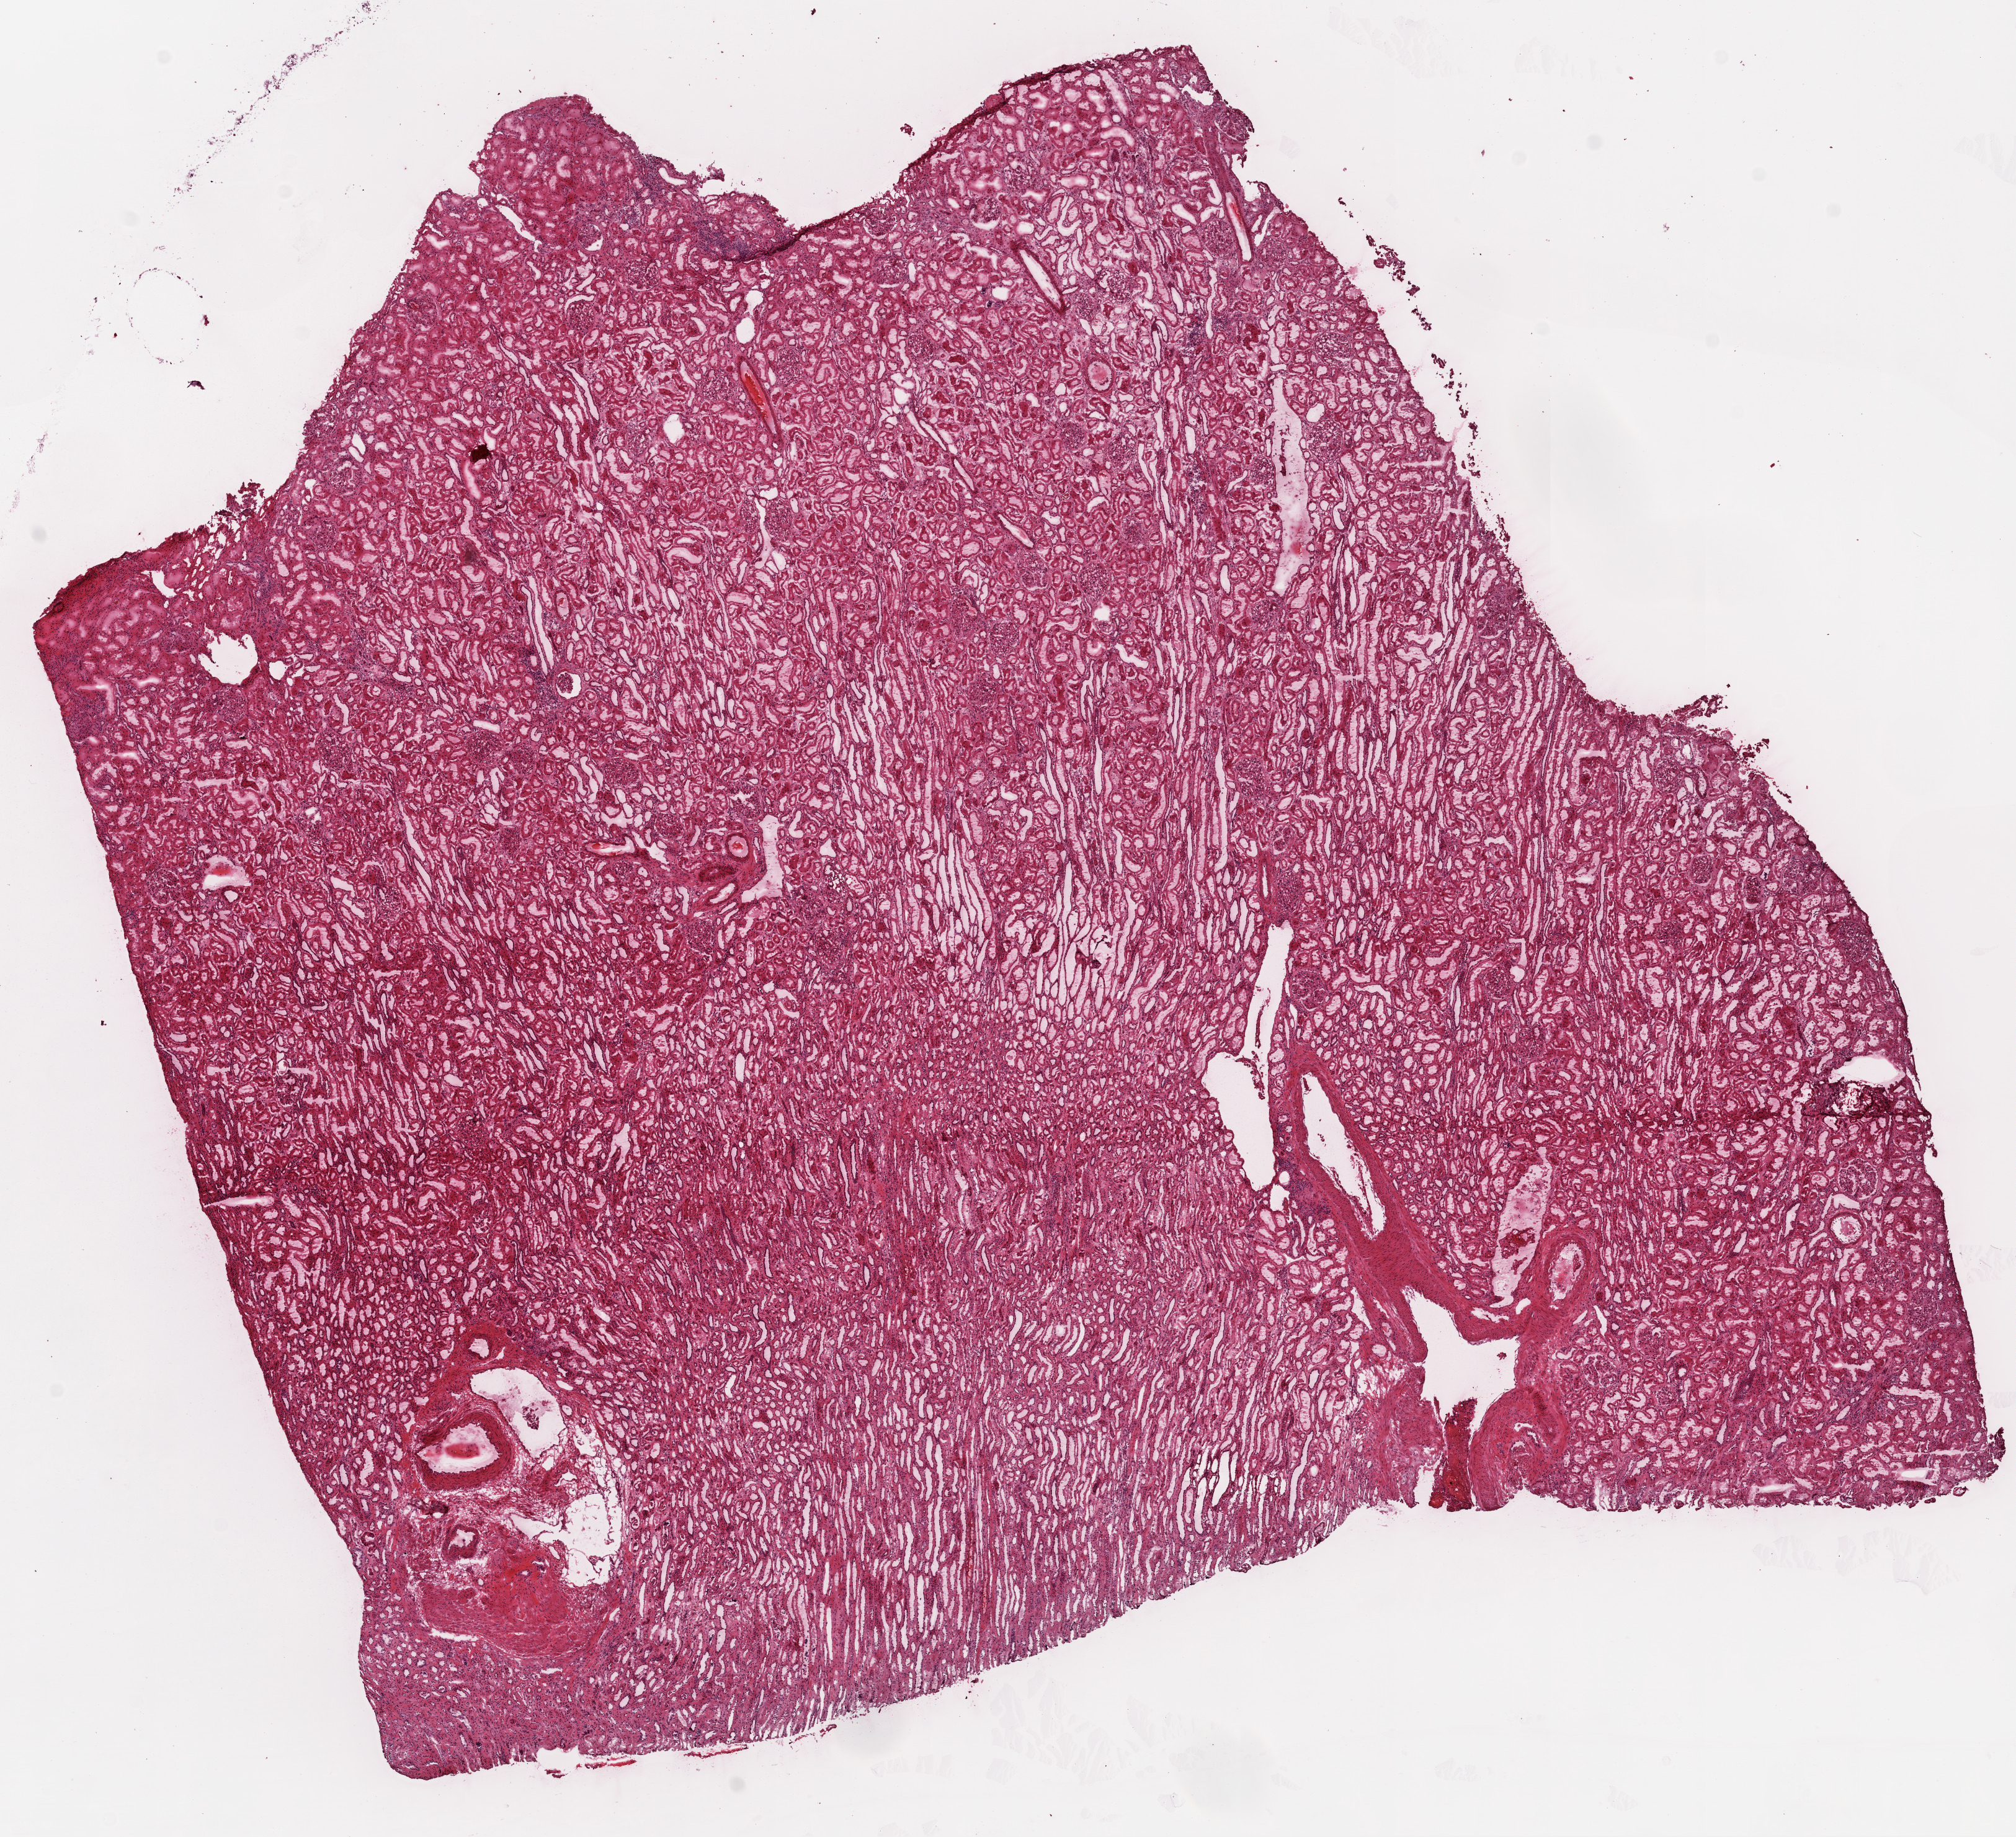
Whole-slide histology image, H&E-stained — whole scanned area (about 13.0 x 11.9 mm, from a 20x scan) shown as a low-resolution overview; frozen section from the top of the tissue portion; kidney, solid tissue normal (non-tumour tissue) sample. Patient: male, age at initial diagnosis 40 years.
This section: solid tissue normal (non-tumour) sample from the same patient. Patient diagnosis: Clear cell adenocarcinoma, NOS.